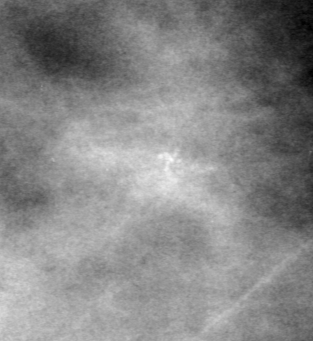
Region of interest cut from a scanned film mammogram (one marked finding), right breast, CC view.
Calcifications, morphology amorphous, distribution segmental; BI-RADS assessment category 0; pathology result (as recorded, not read from the image): benign.